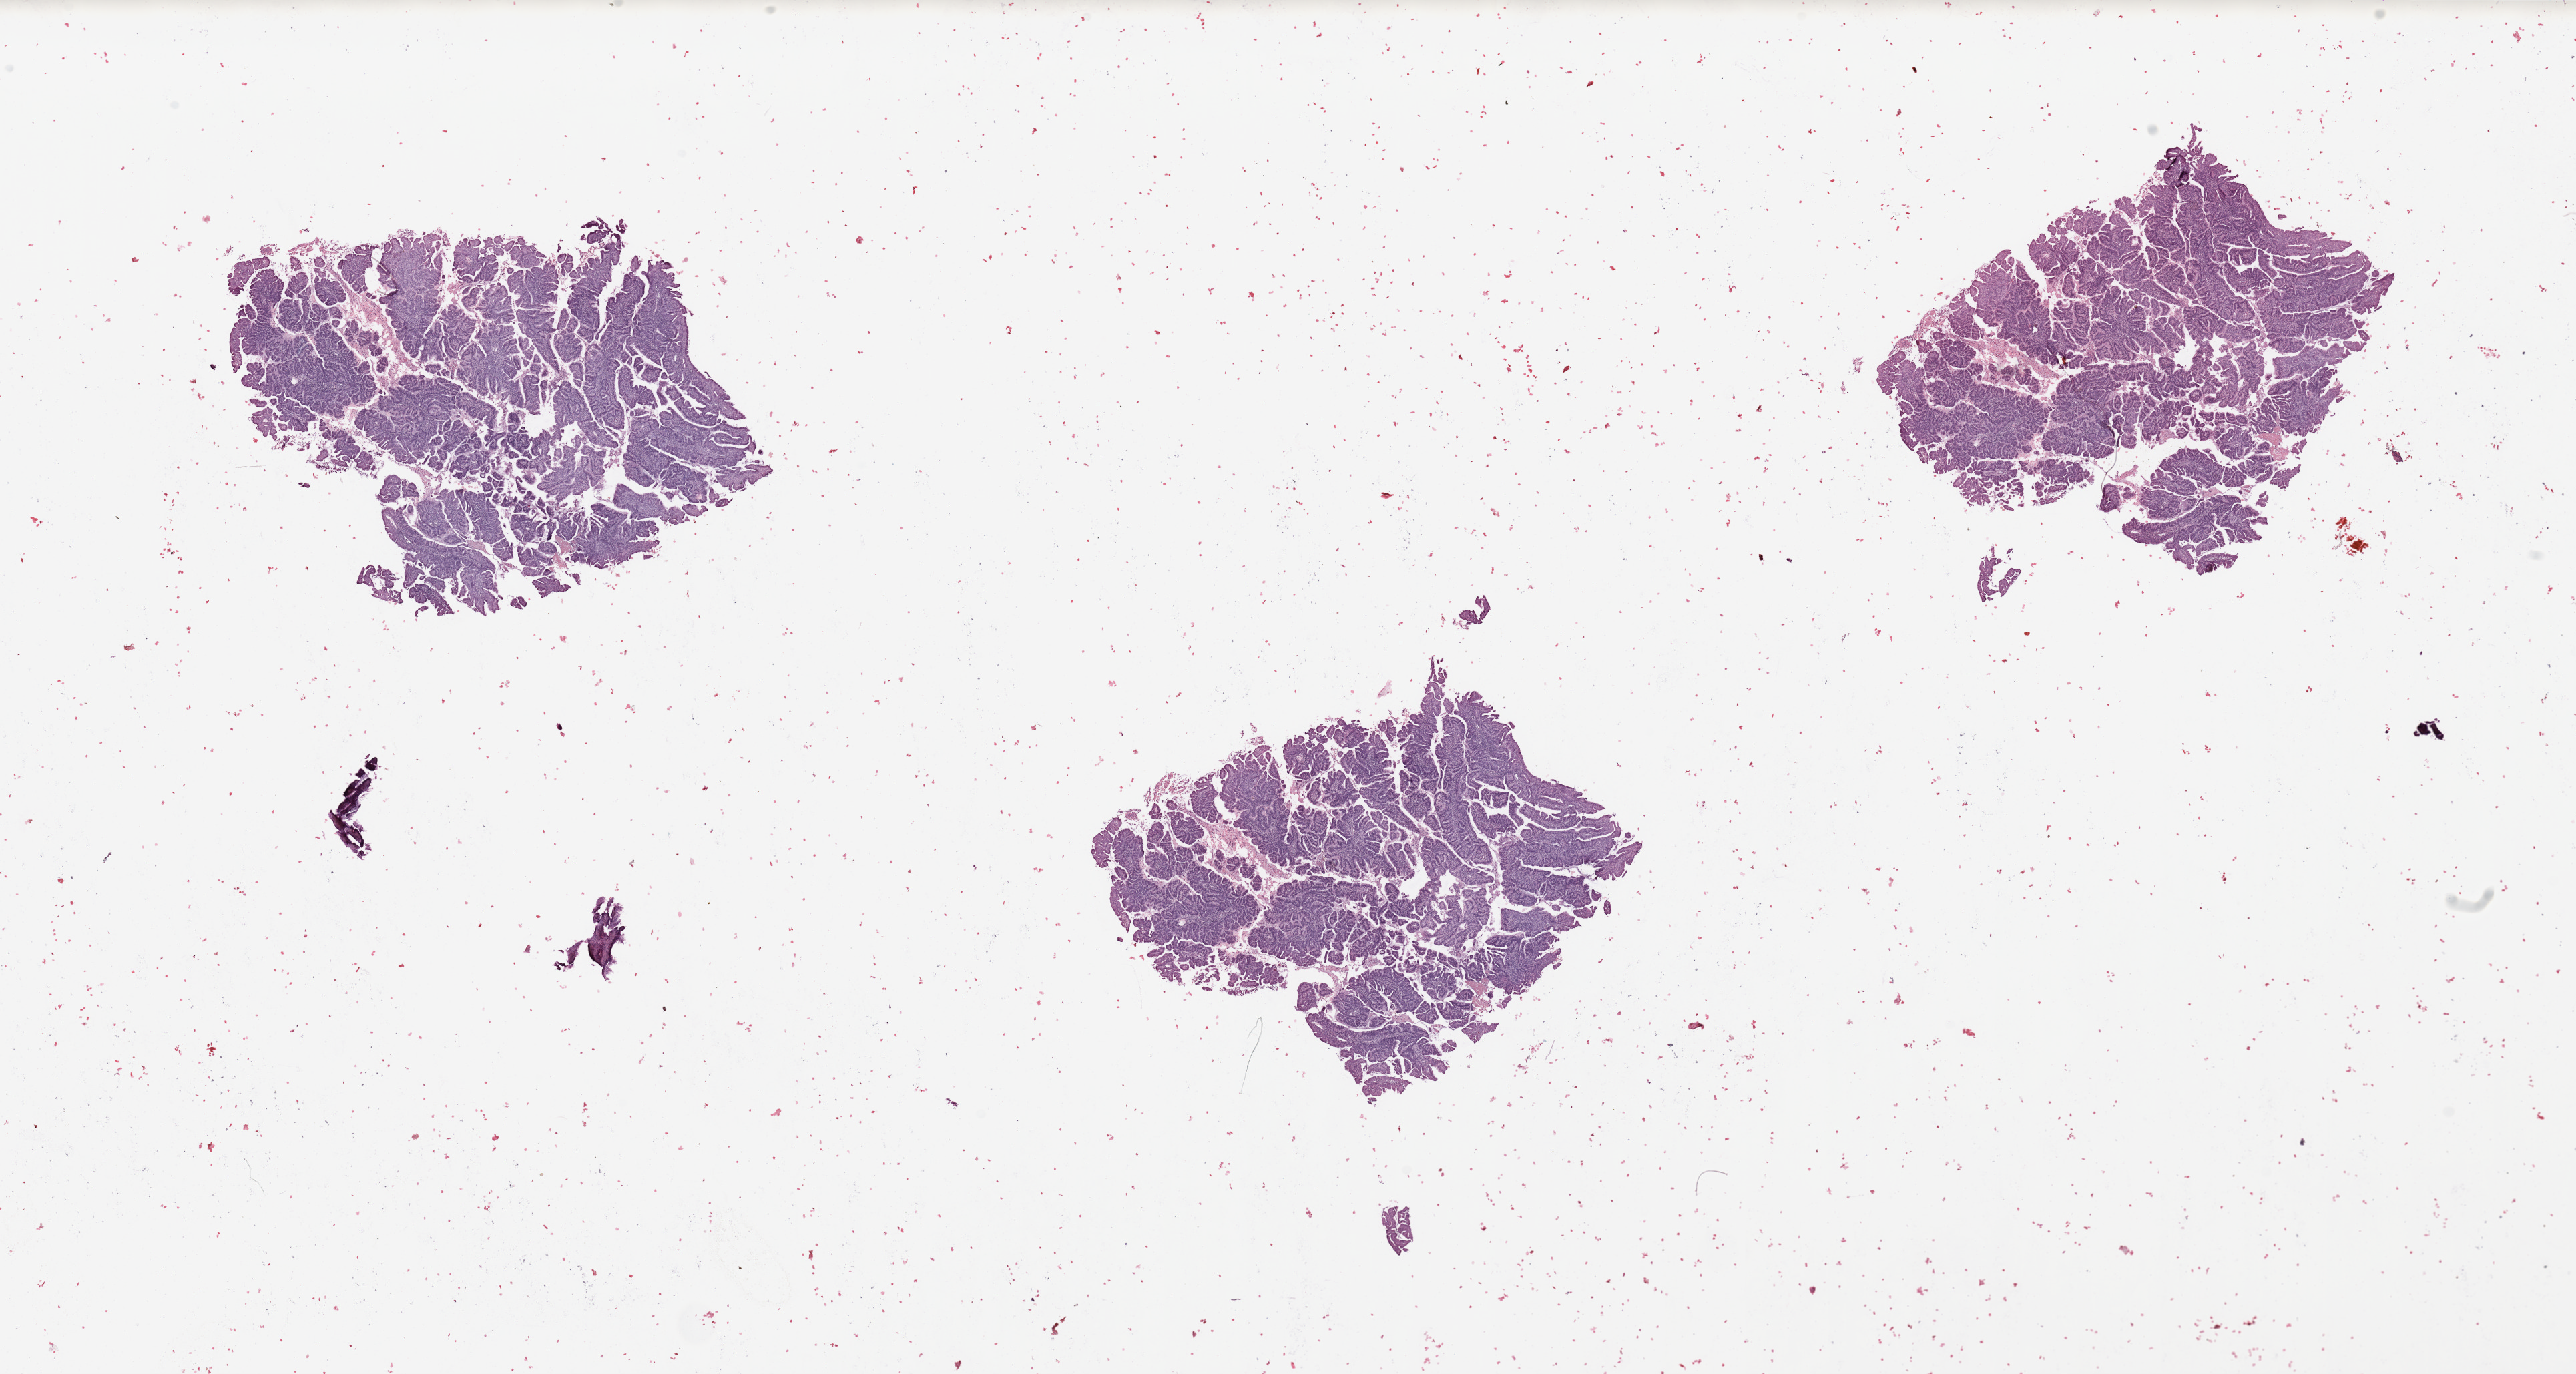
H&E-stained whole-slide image, a low-resolution overview of the entire scanned area, about 30.5 x 16.3 mm (from a 20x scan); tumour tissue sample, sampled site: uterus. 41-year-old female patient.
Histologic diagnosis: Endometrioid adenocarcinoma, NOS.